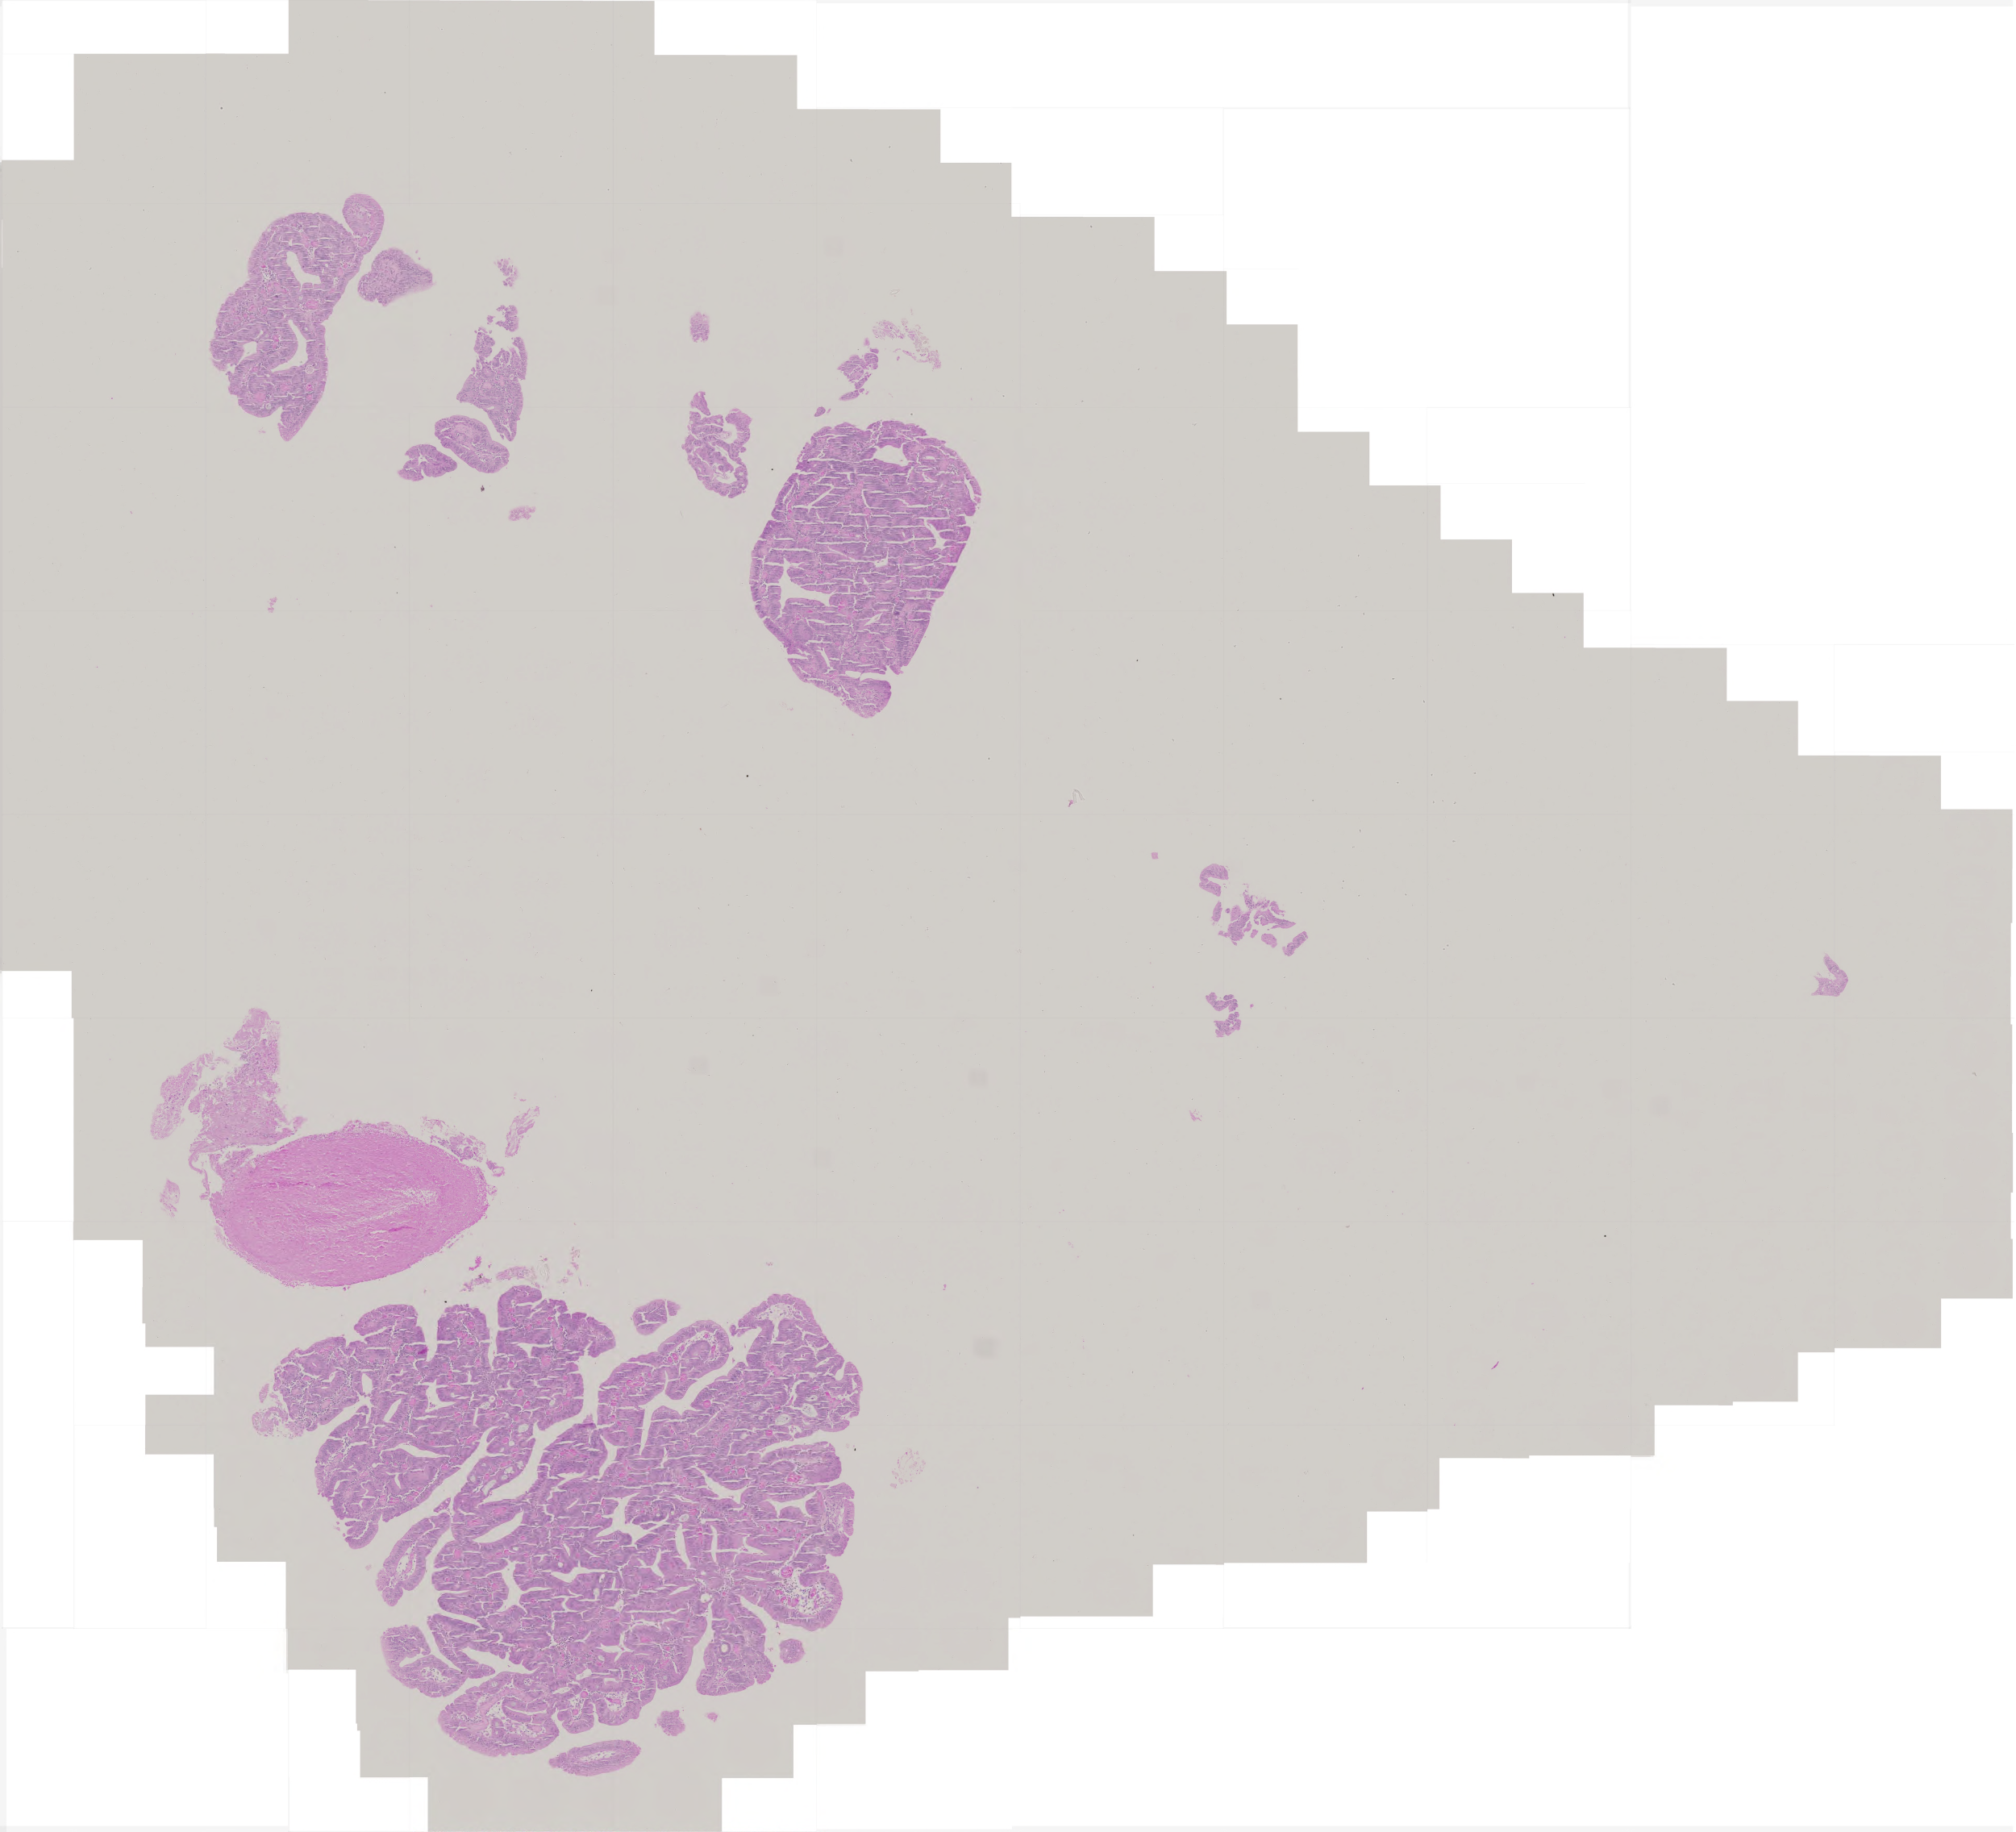
Hematoxylin and eosin (H&E) stained whole-slide image, low-resolution overview of the scanned area, about 5.0 x 4.5 mm. FFPE section. Primary tumour sample from the rectum. Patient sex: female.
TNM: T3 N2 M0. Diagnosis: Adenocarcinoma, NOS. Lymph nodes positive (case pathology): 5 of 18 examined. AJCC pathologic stage: III (5th edition).